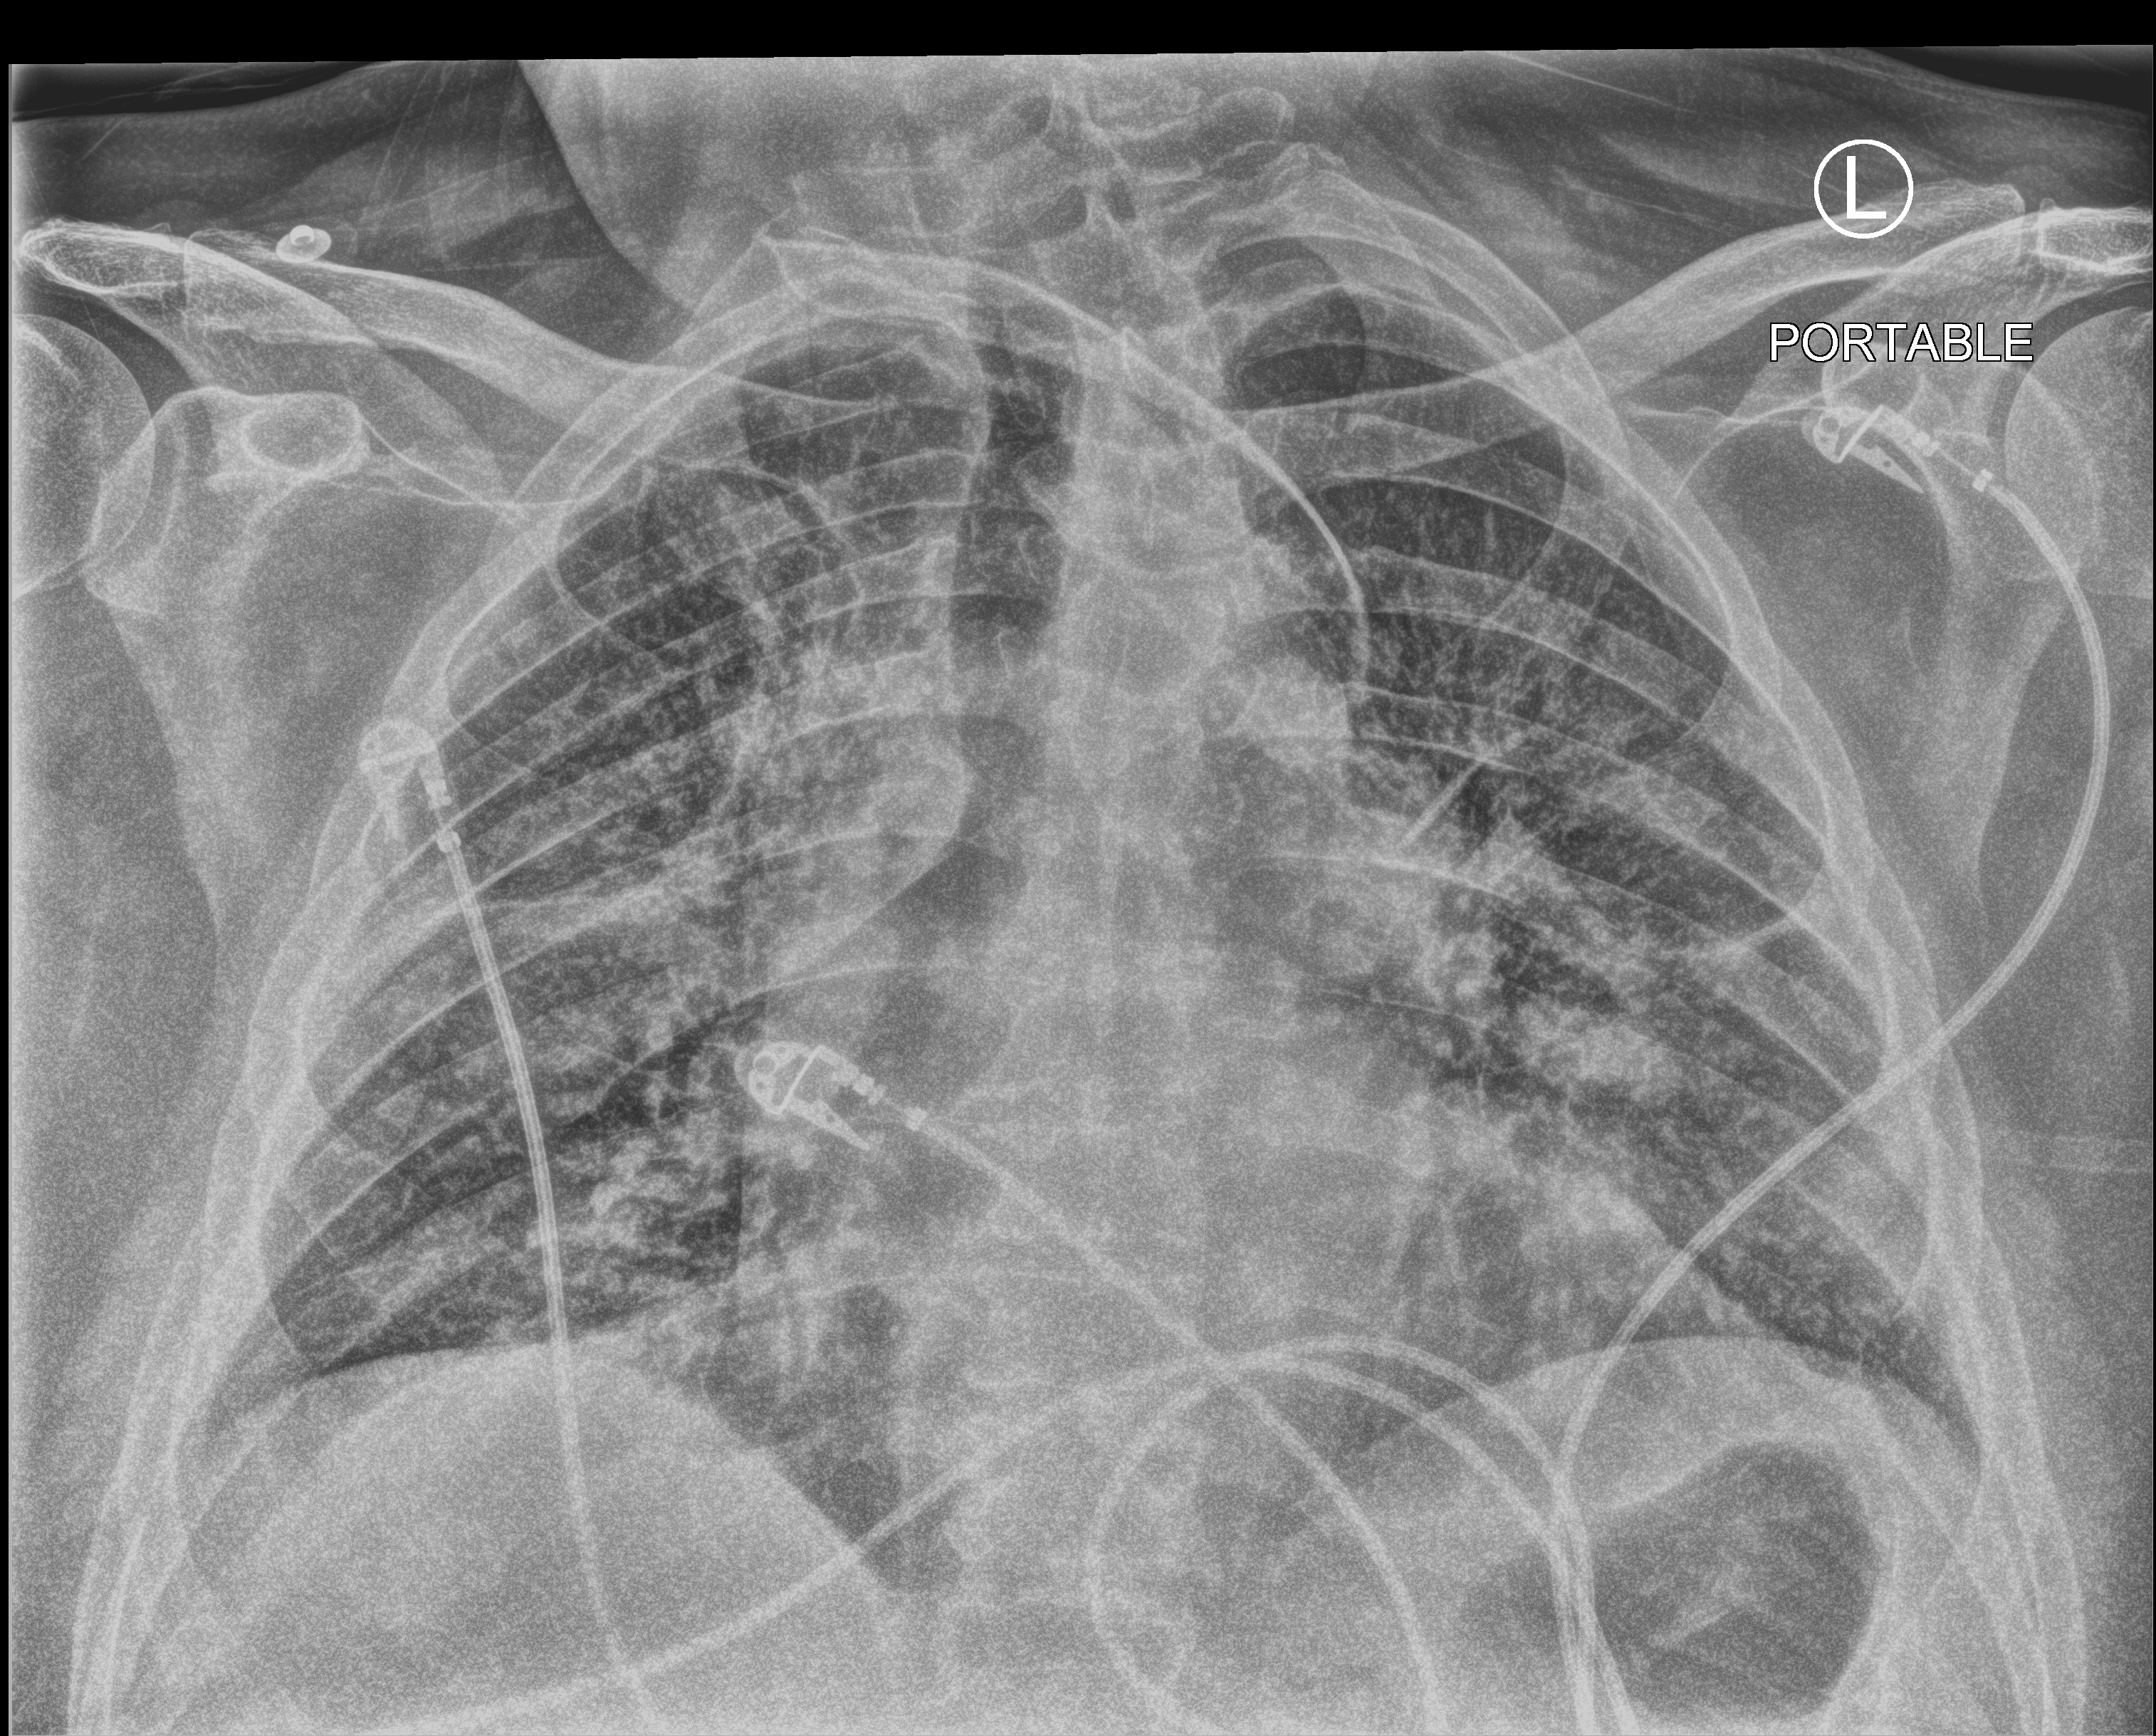
Bedside chest radiograph (computed radiography). Male patient hospitalised with COVID-19, age 60–74 years.
Hospital-stay facts (about this admission, not read from this image; timing relative to this image not recorded): hypertension (admission record): yes; other chronic lung disease (admission record): yes; length of hospital stay: 13 days.